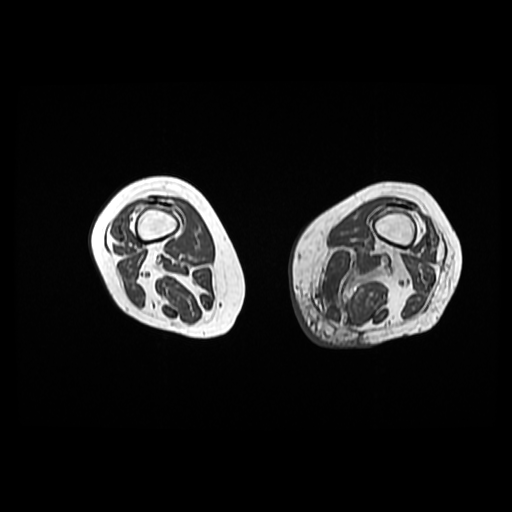
MRI of an extremity soft-tissue mass, one axial slice; 6 mm slice thickness; 512 × 512 image matrix, field of view 420 × 420 mm. Female patient. Case-level facts recorded for this patient, not image findings: histological type: pleomorphic leiomyosarcoma; grade: high; site of the primary tumour: left thigh.
Annotated regions visible in this slice (manually delineated by an expert):
- gross tumour volume including surrounding oedema: bounding box (x1, y1, x2, y2) in pixels: (310, 243, 409, 328)